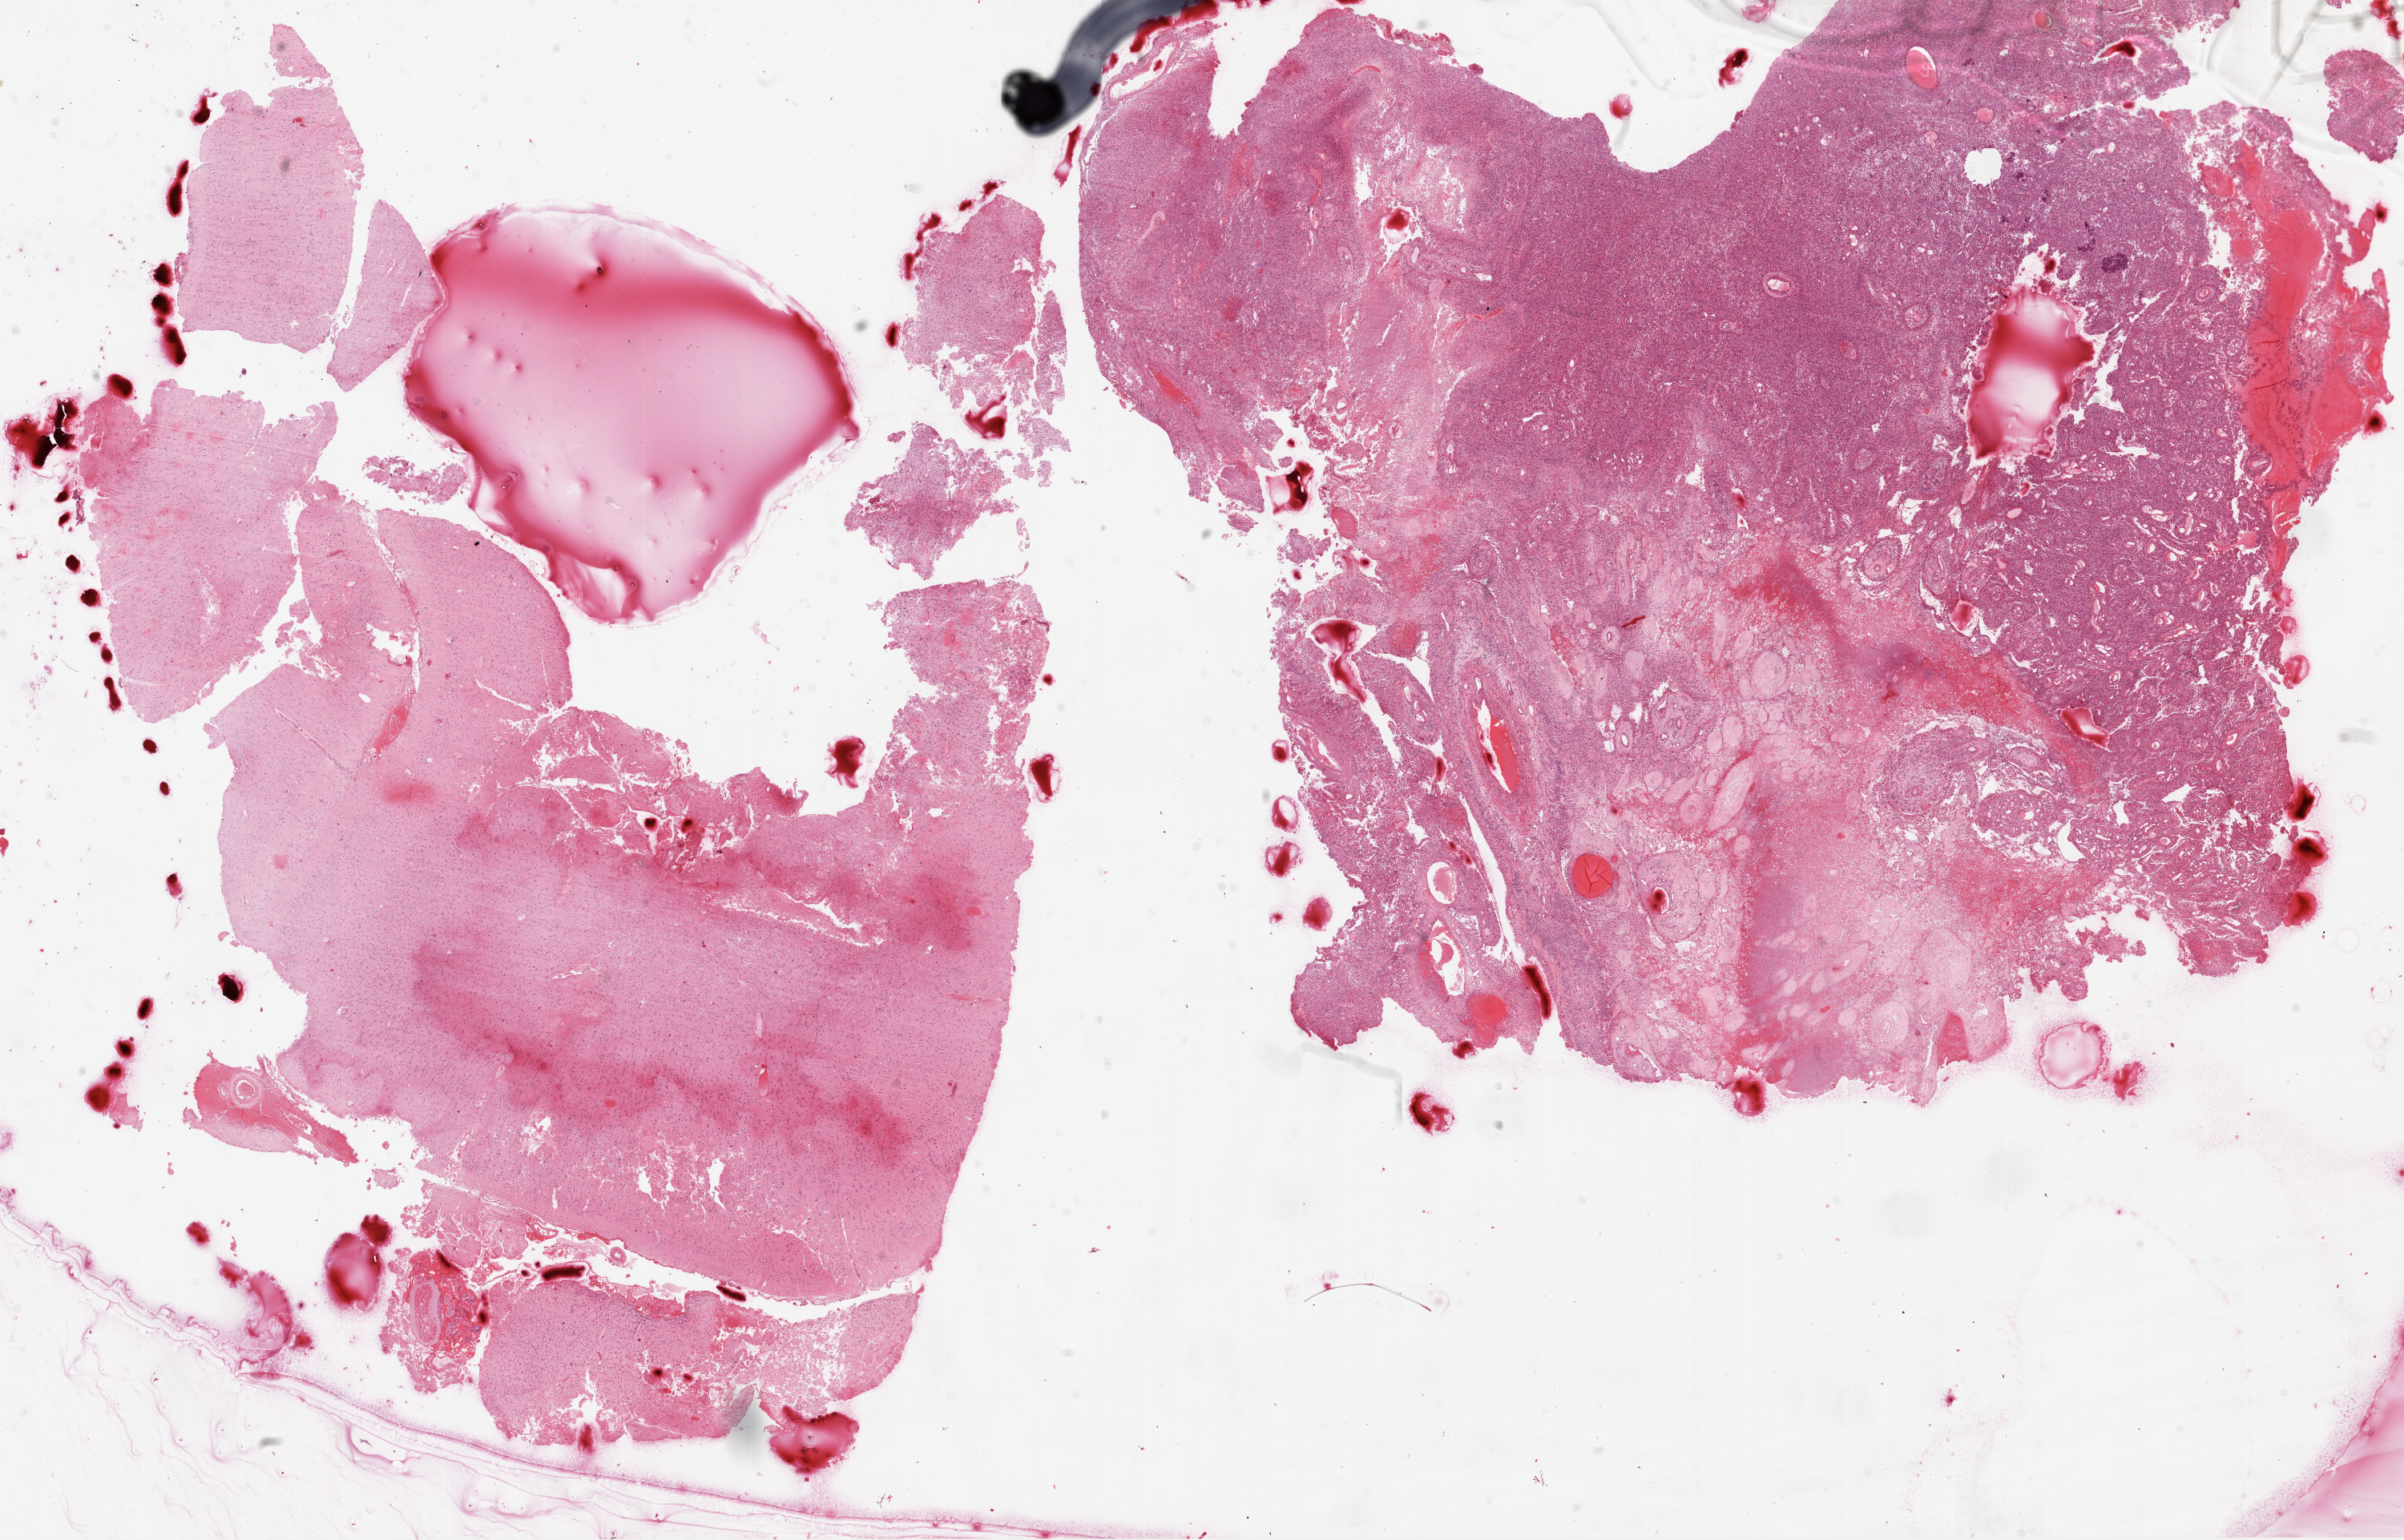
H&E-stained whole-slide image, whole scanned area (about 24.1 x 15.4 mm, from a 20x scan) shown as a low-resolution overview. Formalin-fixed paraffin-embedded (FFPE) diagnostic section. Brain, primary tumour sample. Patient: male, age at initial diagnosis 66 years.
Pathologic diagnosis: Glioblastoma.